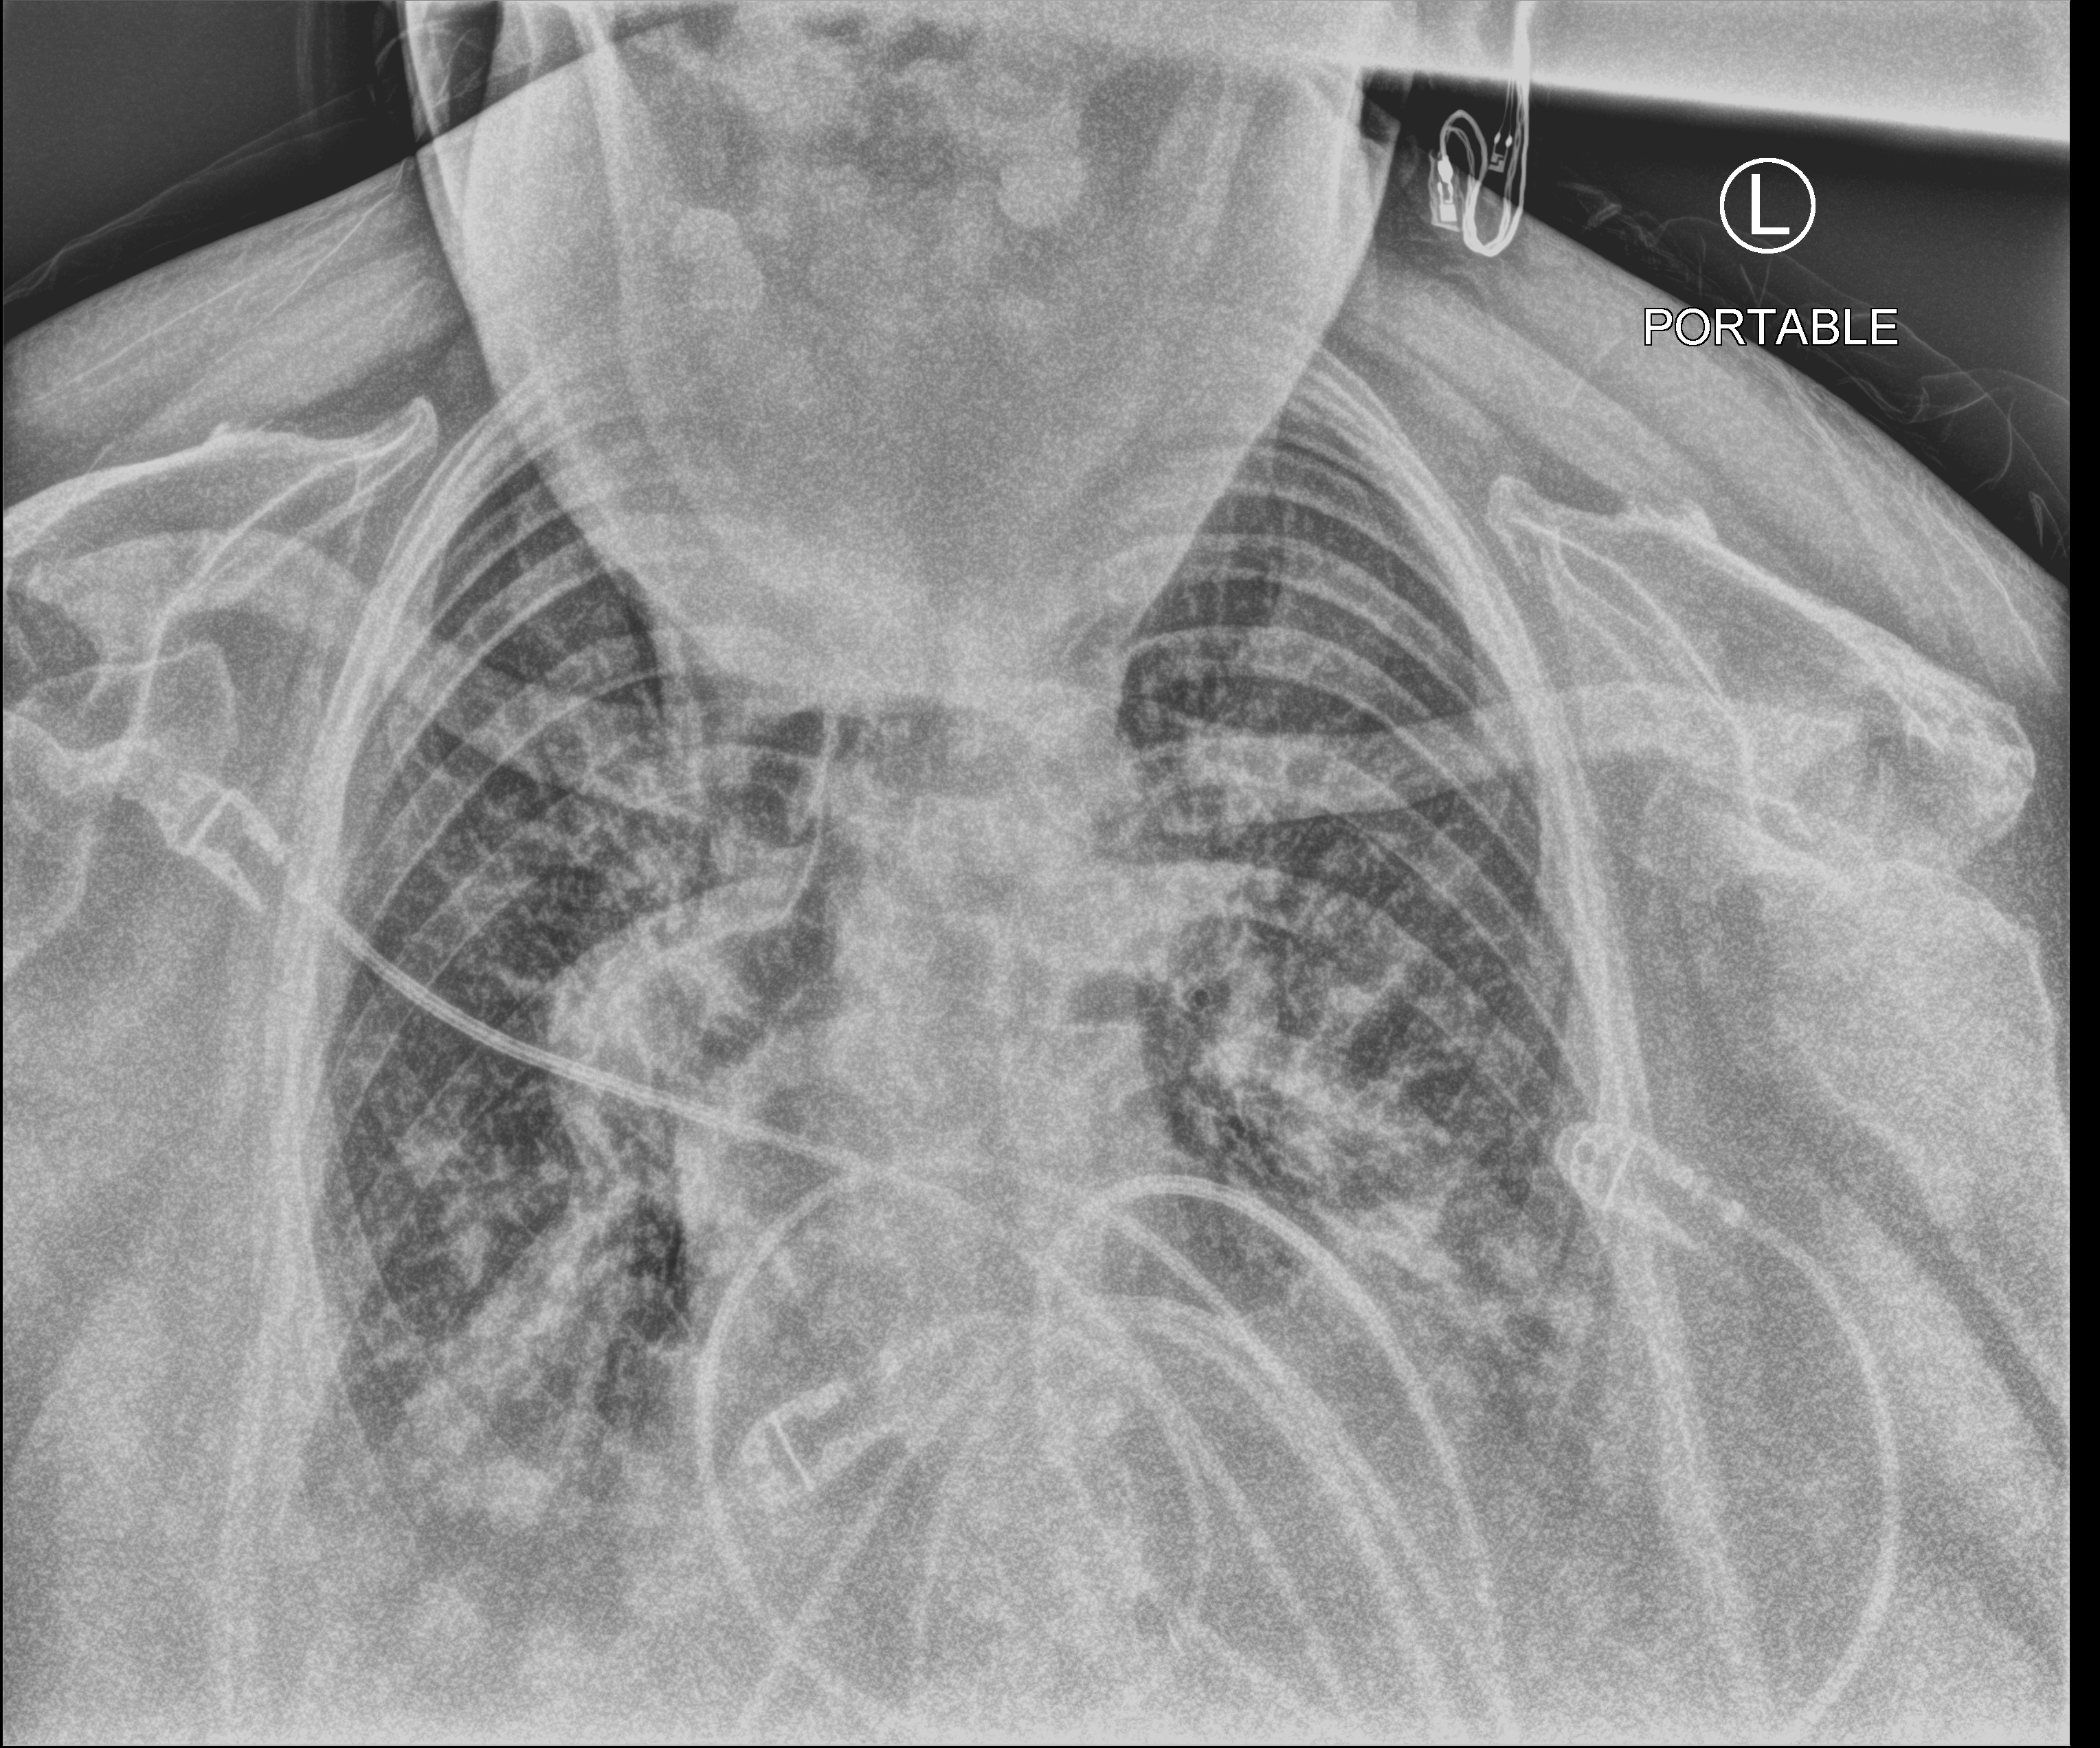
Bedside chest radiograph (computed radiography), anteroposterior (AP) projection. Female patient hospitalised with COVID-19, age 75–90 years.
Hospital-stay facts (about this admission, not read from this image; timing relative to this image not recorded): admitted to intensive care during this hospital stay: no; mechanically ventilated during this hospital stay: no; diabetes (admission record): no.